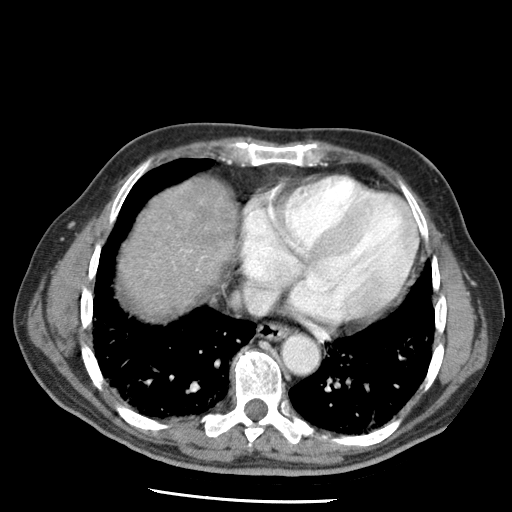
Contrast-enhanced abdominal CT (liver protocol), one axial slice. Position 64 of 79 along the scan axis. Soft-tissue window (W 400 / L 40 HU). 2.5 mm slice thickness. 512 × 512 image matrix. From the clinical record (not read from this slice): diagnosis: hepatocellular carcinoma (patient treated with transarterial chemoembolisation; whether this scan precedes or follows treatment is not stated here); TNM stage (as recorded): Stage-IIIA; Child-Pugh class: A; tumour differentiation: moderately differentiated.
Annotated regions visible in this slice (semi-automatically segmented with operator editing):
- liver parenchyma outside the tumour (the mass and vessels are separate outlines, so this box may not span the whole liver): bounding box <118,178,236,314> (left, top, right, bottom; pixels)
- liver vessels: <180,249,198,270>